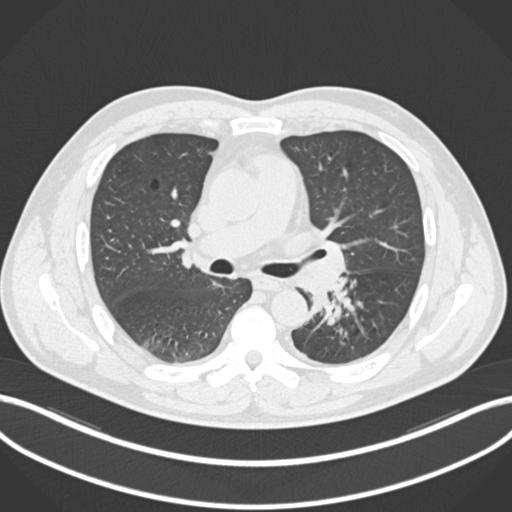
Chest CT, one axial slice. Slice 134 of 223 in the series (ordered by position). 120 kVp. Lung window (W 1500 / L -600 HU). 512 × 512 image matrix, field of view 400 × 400 mm. Patient: male, 50 years. From the clinical record (not read from this slice): clinical TNM (as recorded): T2a N3 M0.
Structures marked on this image (rectangle marked by the reading radiologist):
- lung tumour (recorded histology: squamous cell carcinoma): bounding box <311,277,357,326> (left, top, right, bottom; pixels)